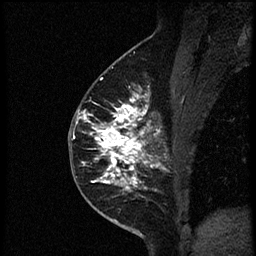
Breast MRI (dynamic contrast-enhanced), one sagittal slice. Position 33 of 56 along the scan axis. Dynamic contrast-enhanced study with each time point stored as its own series, time point 2 of 4 at this slice position (early post-contrast, ordered by acquisition time). 1.5 T. TE 4.2 ms, TR 18.9 ms. 2 mm slice thickness. 256 × 256 image matrix, field of view 200 × 200 mm. Female patient. Case-level facts recorded for this patient, not image findings: setting: breast cancer imaged before/during neoadjuvant chemotherapy; receptor status: HER2-positive.
Outlined on this slice (semi-automatically segmented with operator editing):
- analysis volume of interest (the breast-tissue region the enhancement analysis was run in; not a lesion): bounding box (x1, y1, x2, y2) in pixels: (78, 85, 174, 189)
- tumour enhancement mask (voxels above the 100 % enhancement threshold inside the analysis volume of interest): (82, 95, 164, 189)